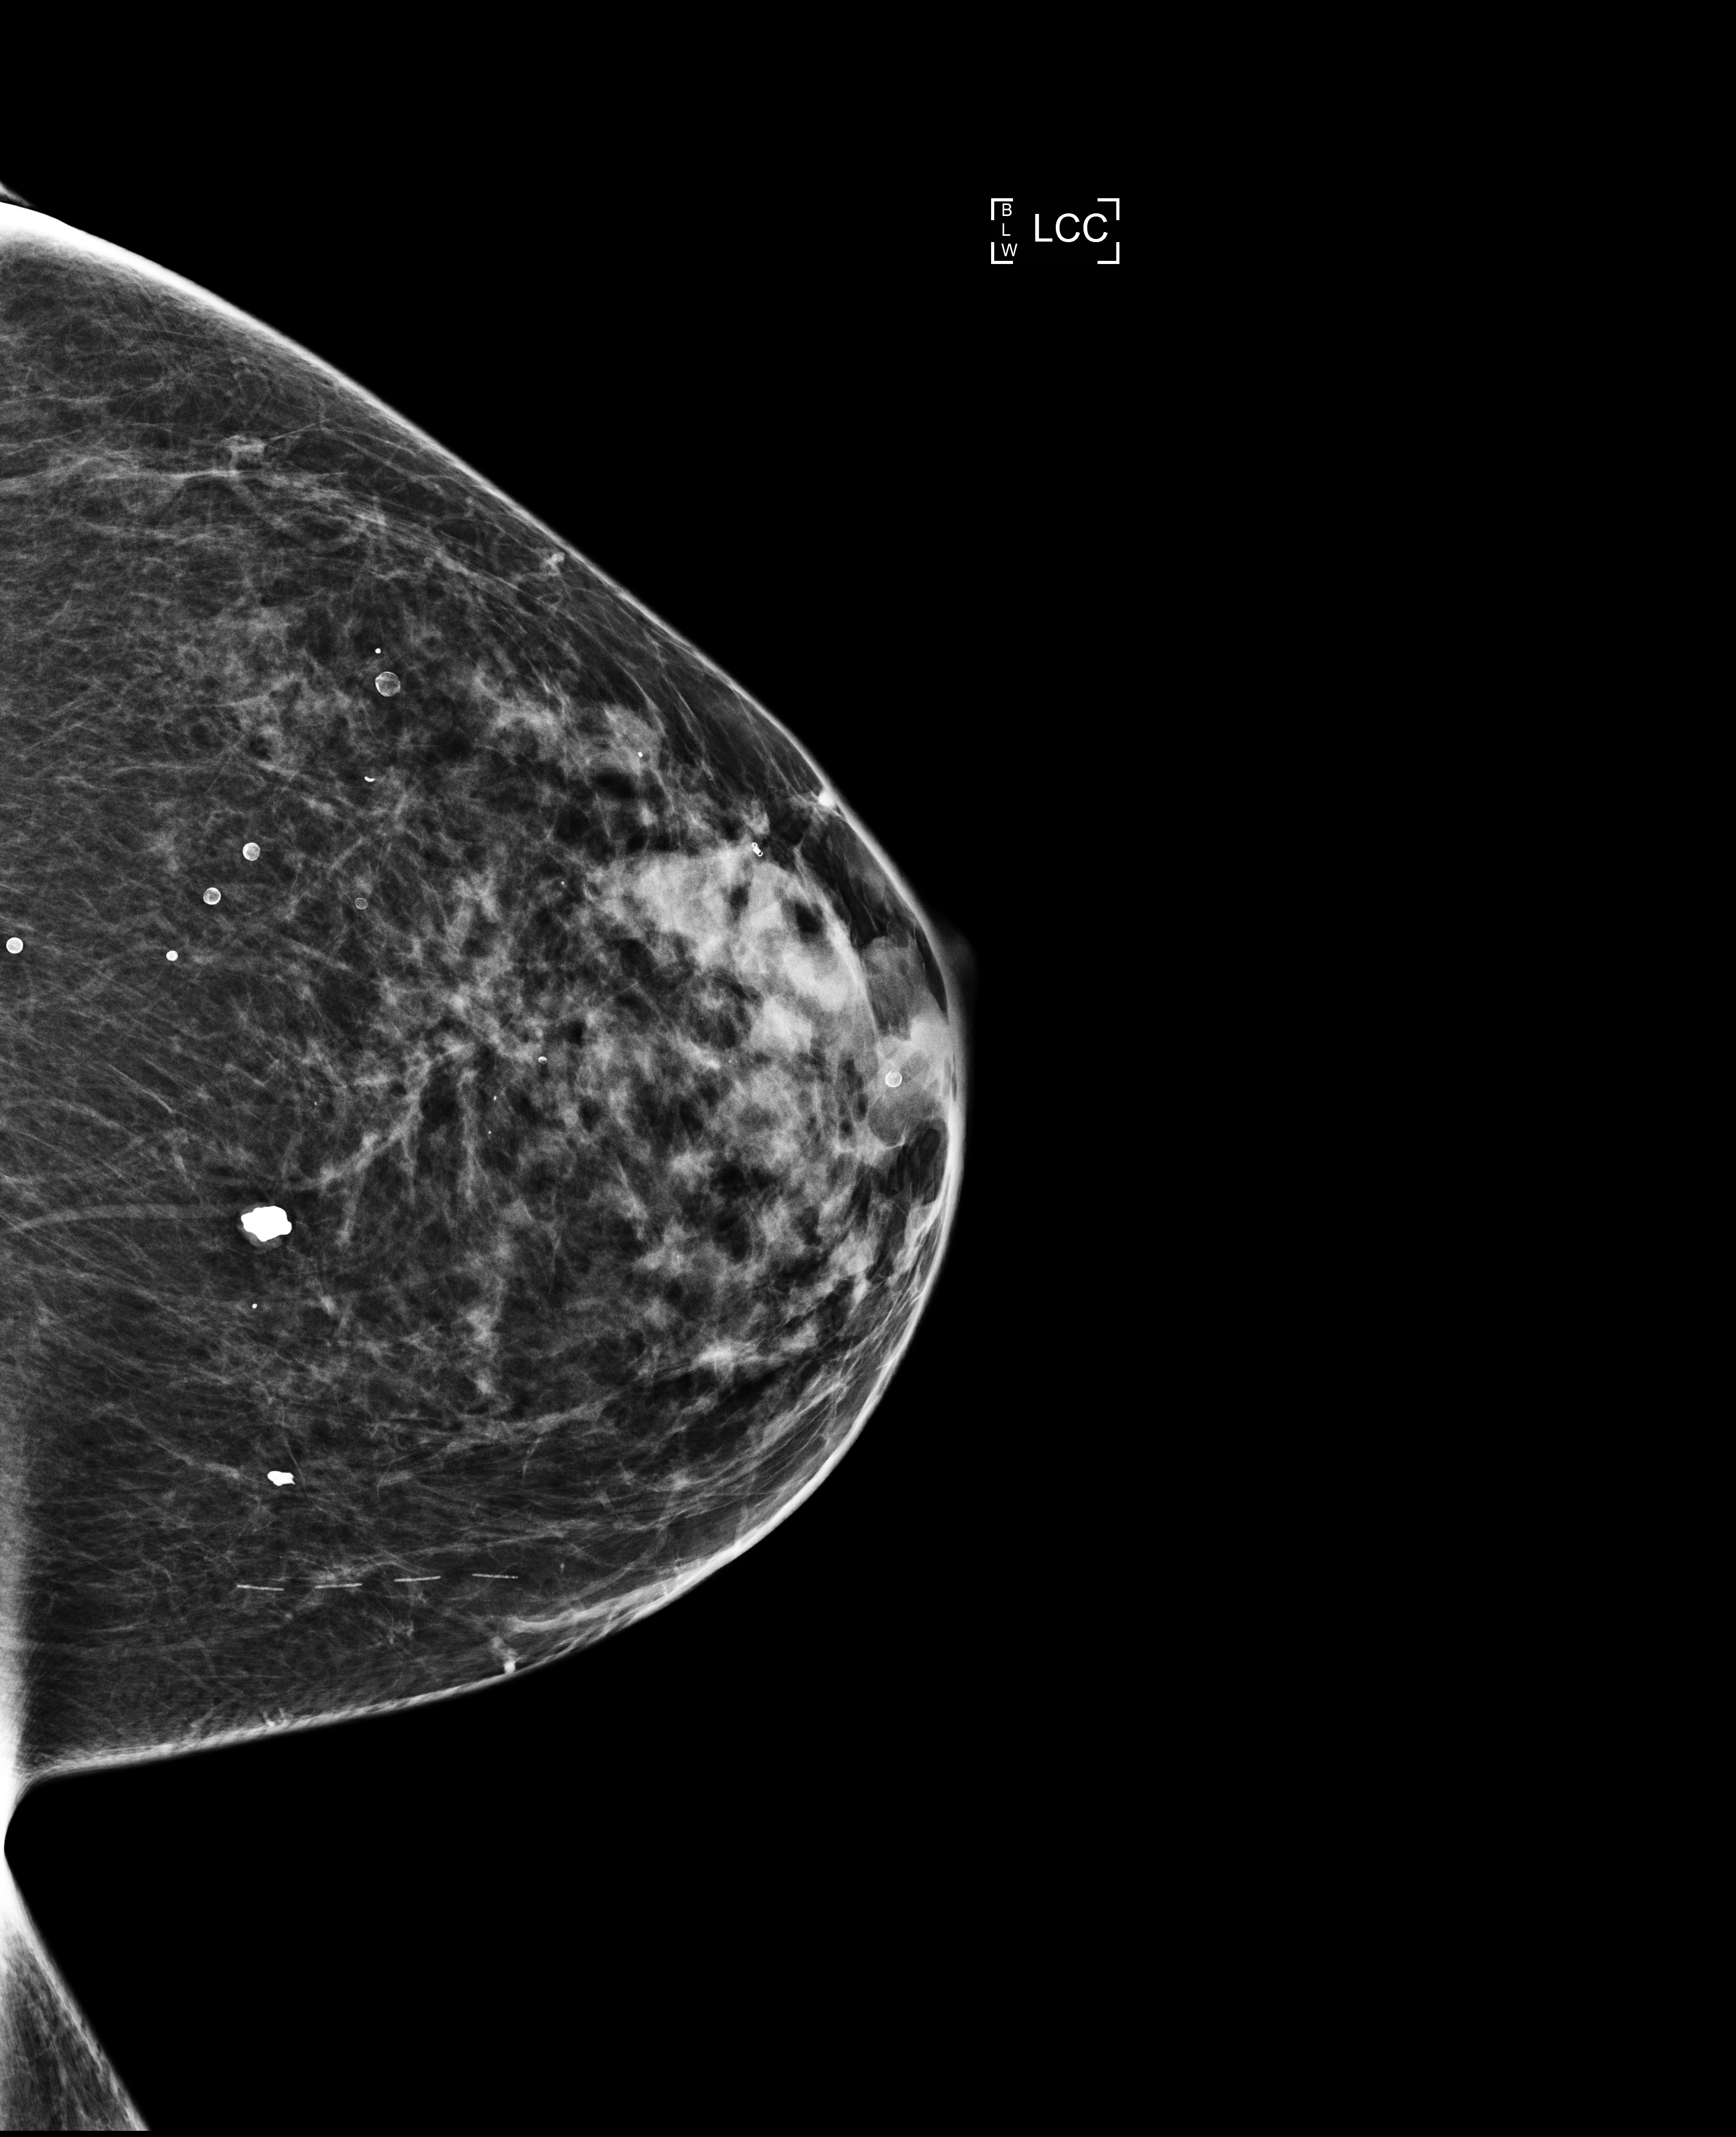
Annual screening mammography examination, compressed breast thickness 38 mm, system: Selenia Dimensions. Female patient, age 69 years.
Image type: full-field digital mammogram. Breast: left. Projection: CC view.